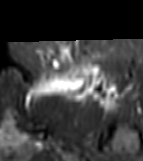
MRI of an extremity soft-tissue mass, one axial slice; position 47 of 81 along the scan axis; STIR; MR volume resampled by the dataset authors to the PET/CT grid (not the native acquisition matrix); 3.27 mm slice thickness; 143 × 161 image matrix. Female patient. Case-level facts recorded for this patient, not image findings: histological type: myxofibrosarcoma; grade: intermediate; site of the primary tumour: left thigh.
Outlined on this slice (expert contour drawn on MRI and transferred to this co-registered scan by the dataset authors):
- gross tumour volume including surrounding oedema: bounding box [x1, y1, x2, y2] px = [22, 63, 123, 107]